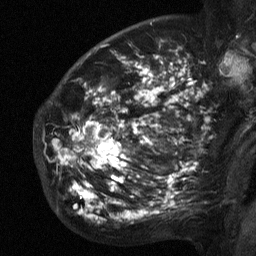
Breast MRI (dynamic contrast-enhanced), one sagittal slice; position 41 of 64 along the scan axis; dynamic contrast-enhanced study with each time point stored as its own series, time point 2 of 3 at this slice position (early post-contrast, ordered by acquisition time); 1.5 T; TE 4.8 ms, TR 27 ms; 256 × 256 image matrix, field of view 200 × 200 mm. Patient: female, 50 years. Case-level facts recorded for this patient, not image findings: setting: breast cancer imaged before/during neoadjuvant chemotherapy; receptor status: HER2-positive.
Outlined on this slice (semi-automatic segmentation, software-assisted and operator-edited):
- analysis volume of interest (the breast-tissue region the enhancement analysis was run in; not a lesion): bounding box [x1, y1, x2, y2] px = [53, 64, 211, 218]
- tumour enhancement mask (voxels above the 90 % enhancement threshold inside the analysis volume of interest): [55, 64, 195, 218]